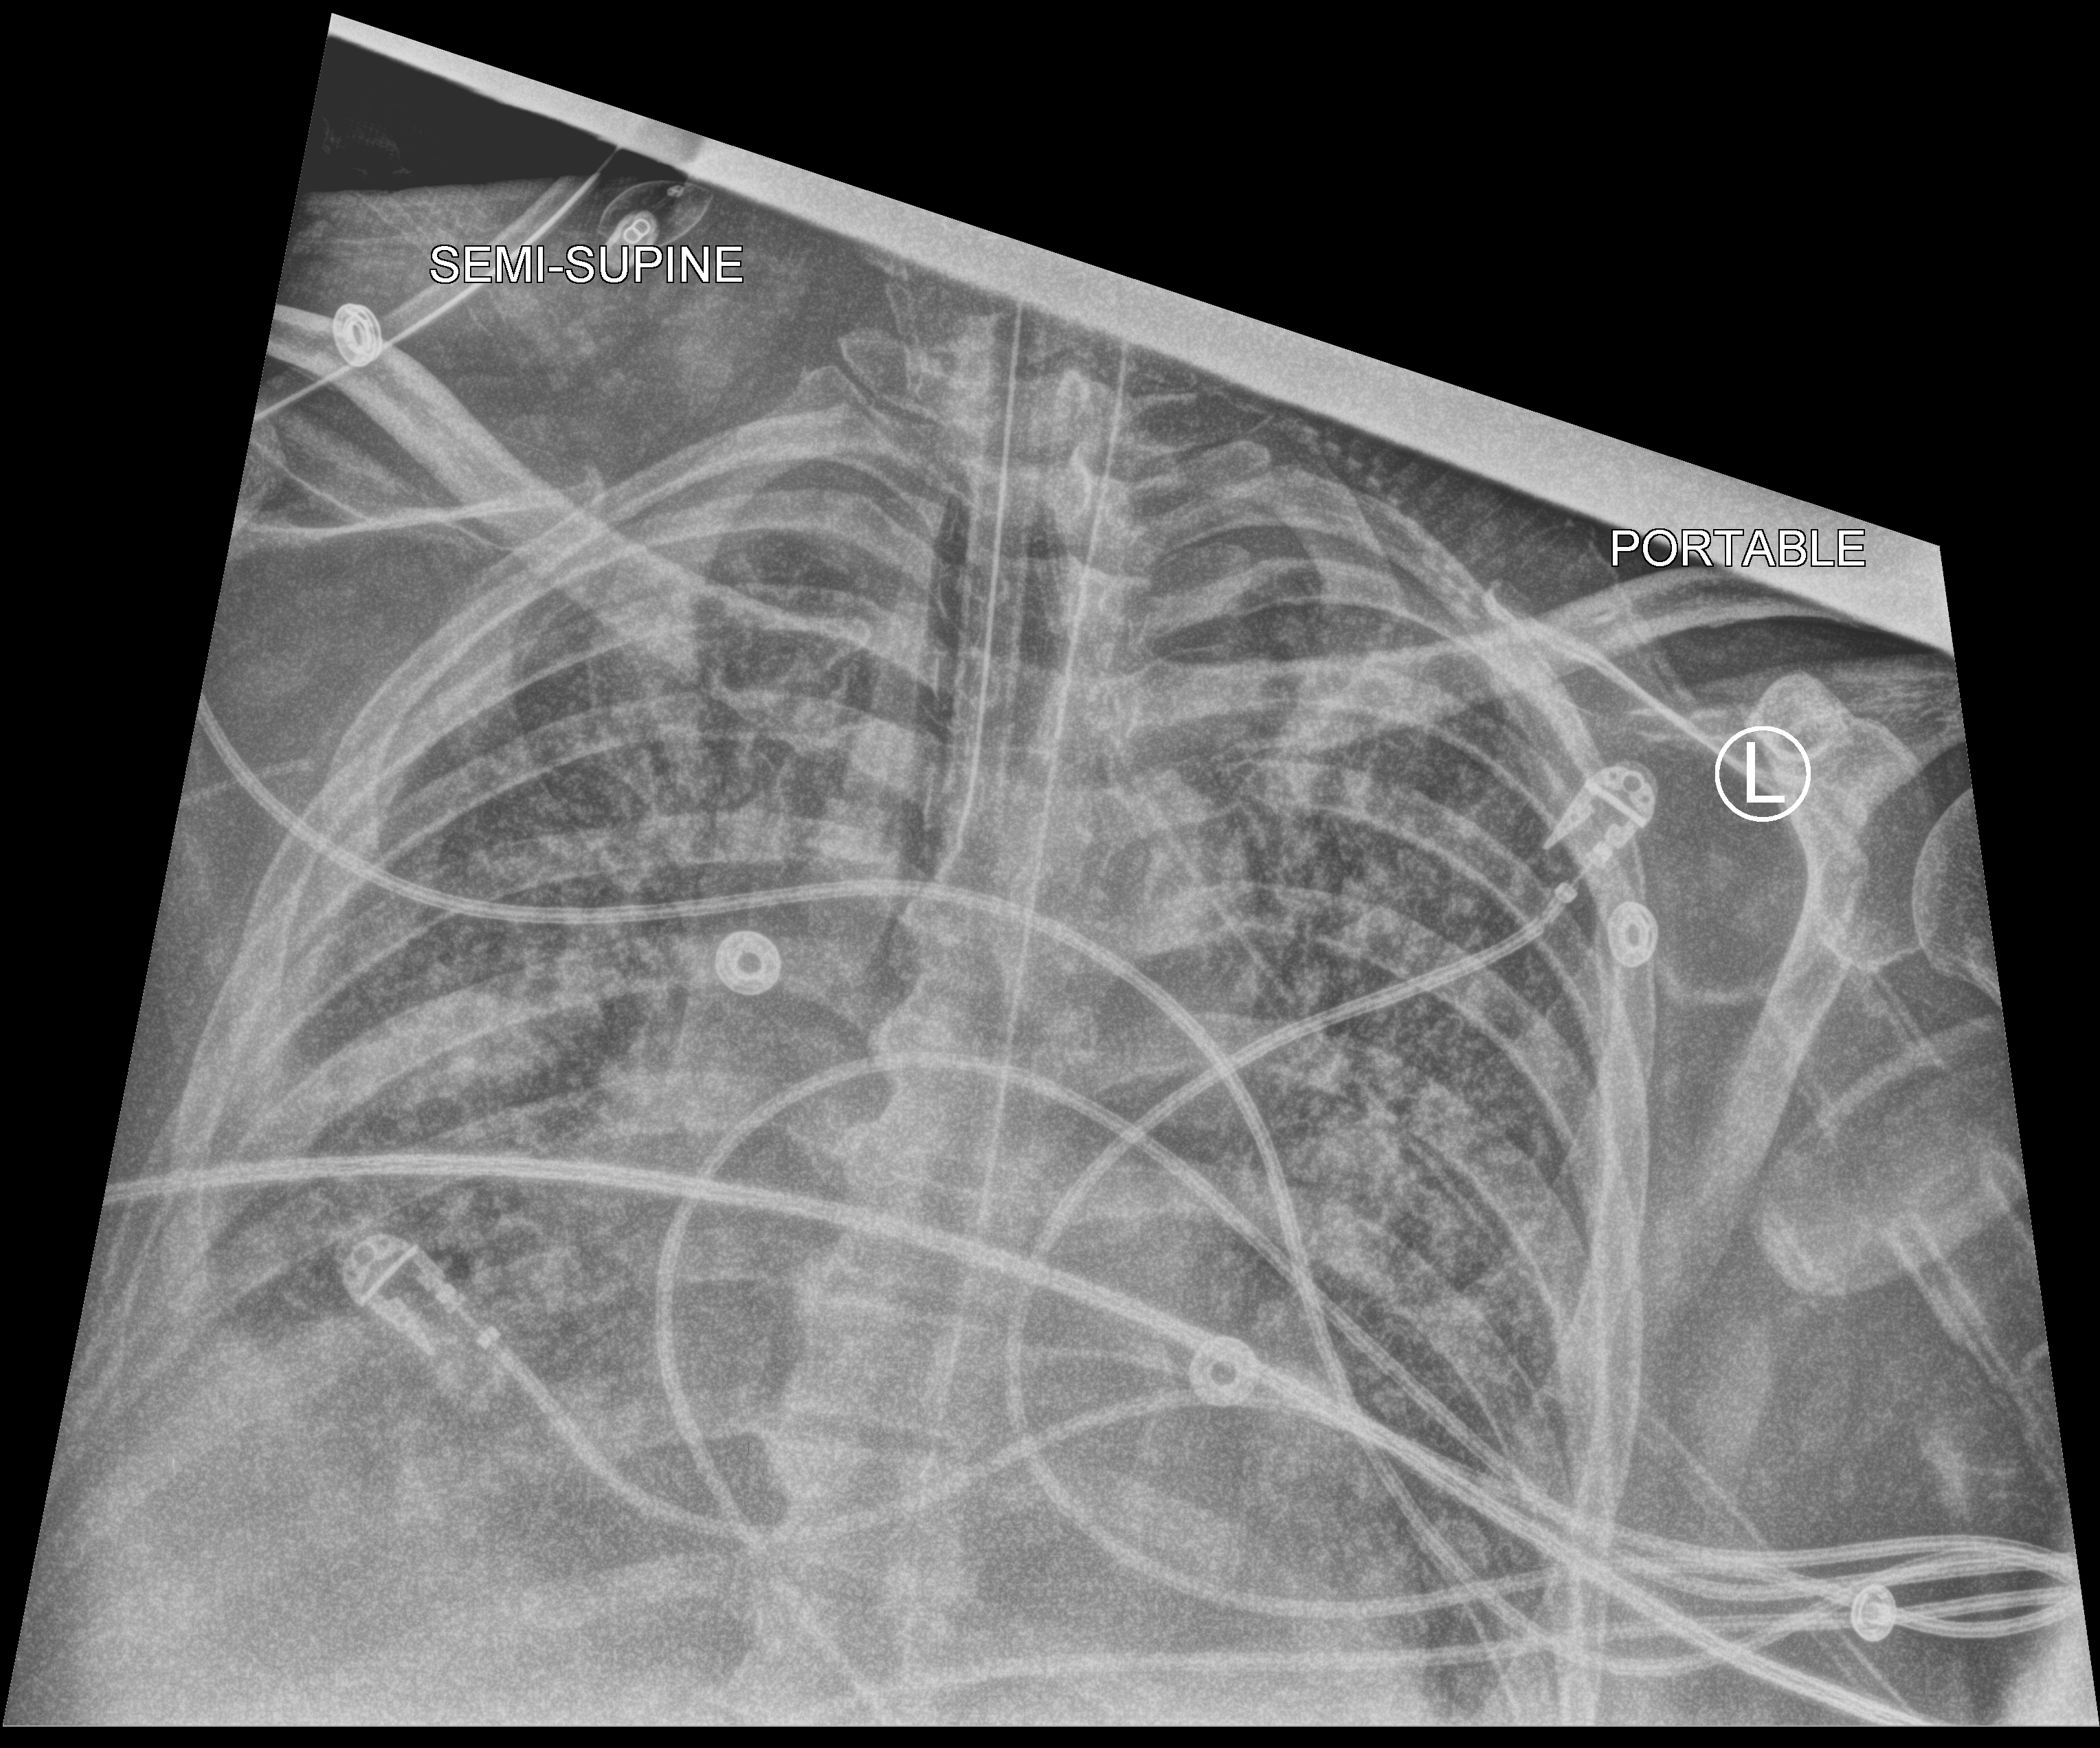
Portable chest radiograph; anteroposterior (AP) projection. Male patient hospitalised with COVID-19, age 60–74 years.
Admission-level facts for this patient (not findings on this image; timing relative to this image not recorded): admitted to intensive care during this hospital stay: yes; hypertension (admission record): yes.